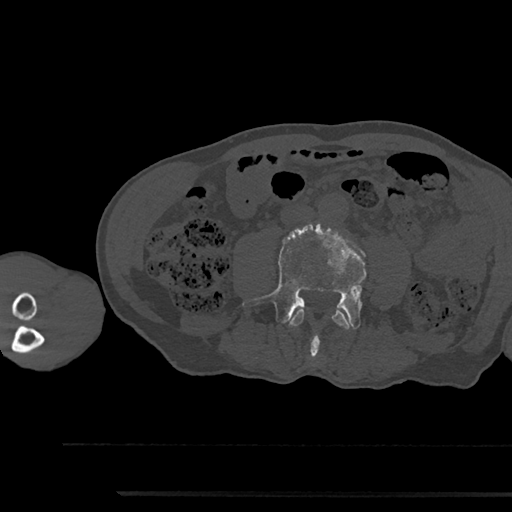
CT including the spine, one axial slice; position 434 of 797 along the scan axis; bone window (W 1800 / L 400 HU); 0.5 mm slice thickness; 512 × 512 image matrix, field of view 367 × 367 mm. Male patient, age 79 years. Case-level facts recorded for this patient, not image findings: primary cancer: prostate.
Structures marked on this image (semi-automatic segmentation, software-assisted and operator-edited):
- L3 vertebra: bounding box [x1, y1, x2, y2] px = [289, 308, 350, 329]
- L4 vertebra: [243, 225, 366, 356]